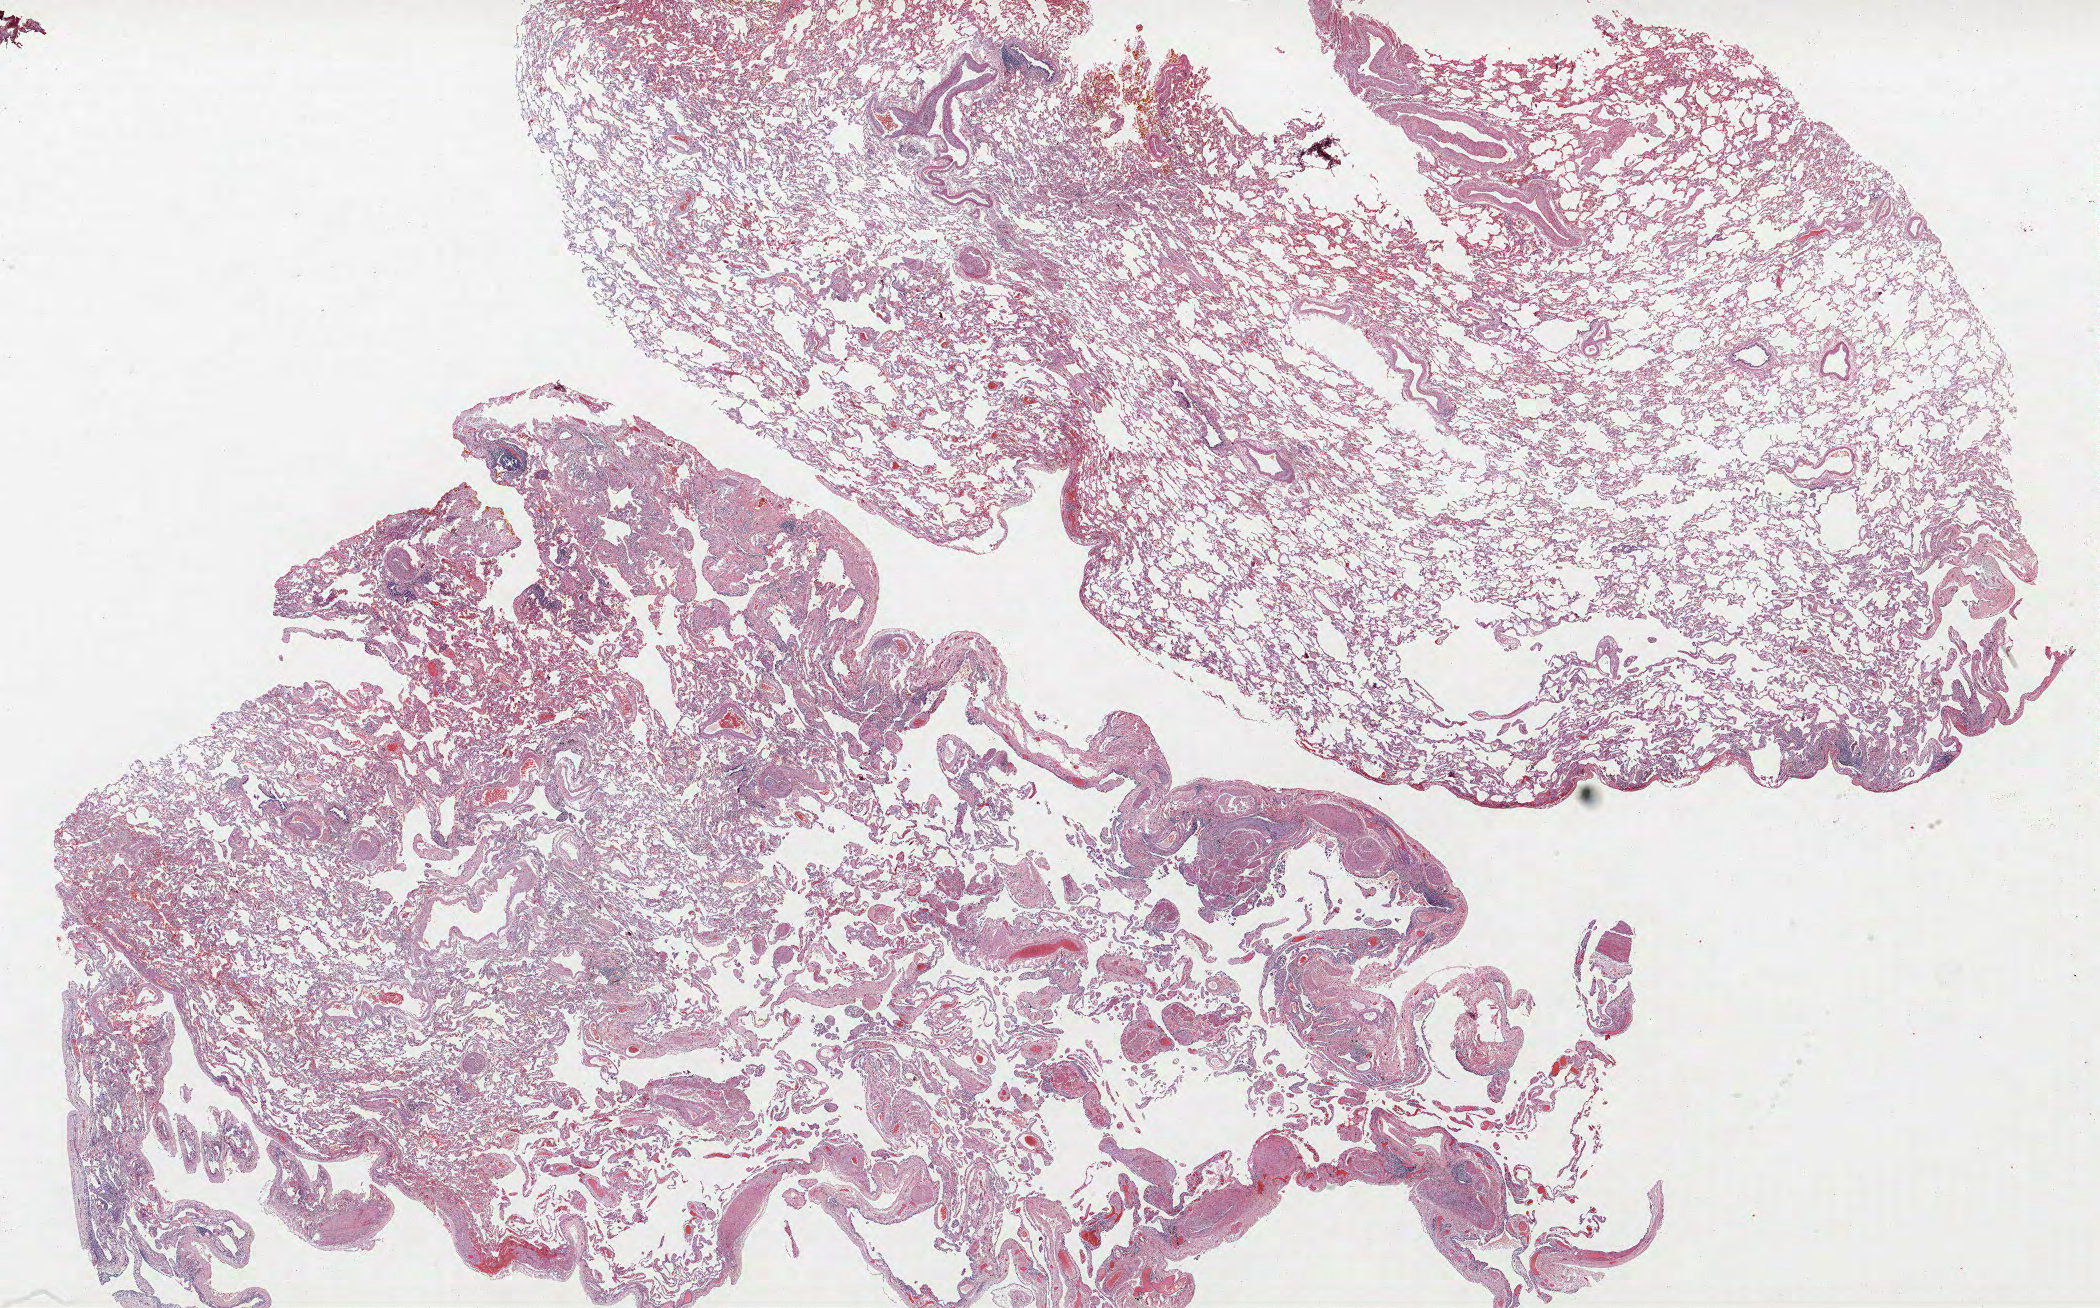
Whole-slide histology image, H&E-stained — shown as a low-resolution overview of the whole scanned area (about 33.6 x 20.9 mm, from a 40x scan). FFPE section. Lung. Male, age 56 at enrolment. Former smoker at enrolment. Grade: moderately differentiated (G2).
- primary tumour location (clinical record): right upper lobe
- stage (AJCC 6th edition): IA
- tumour size (pathology): 9 mm
- participant's lung-cancer diagnosis: Adenocarcinoma, NOS